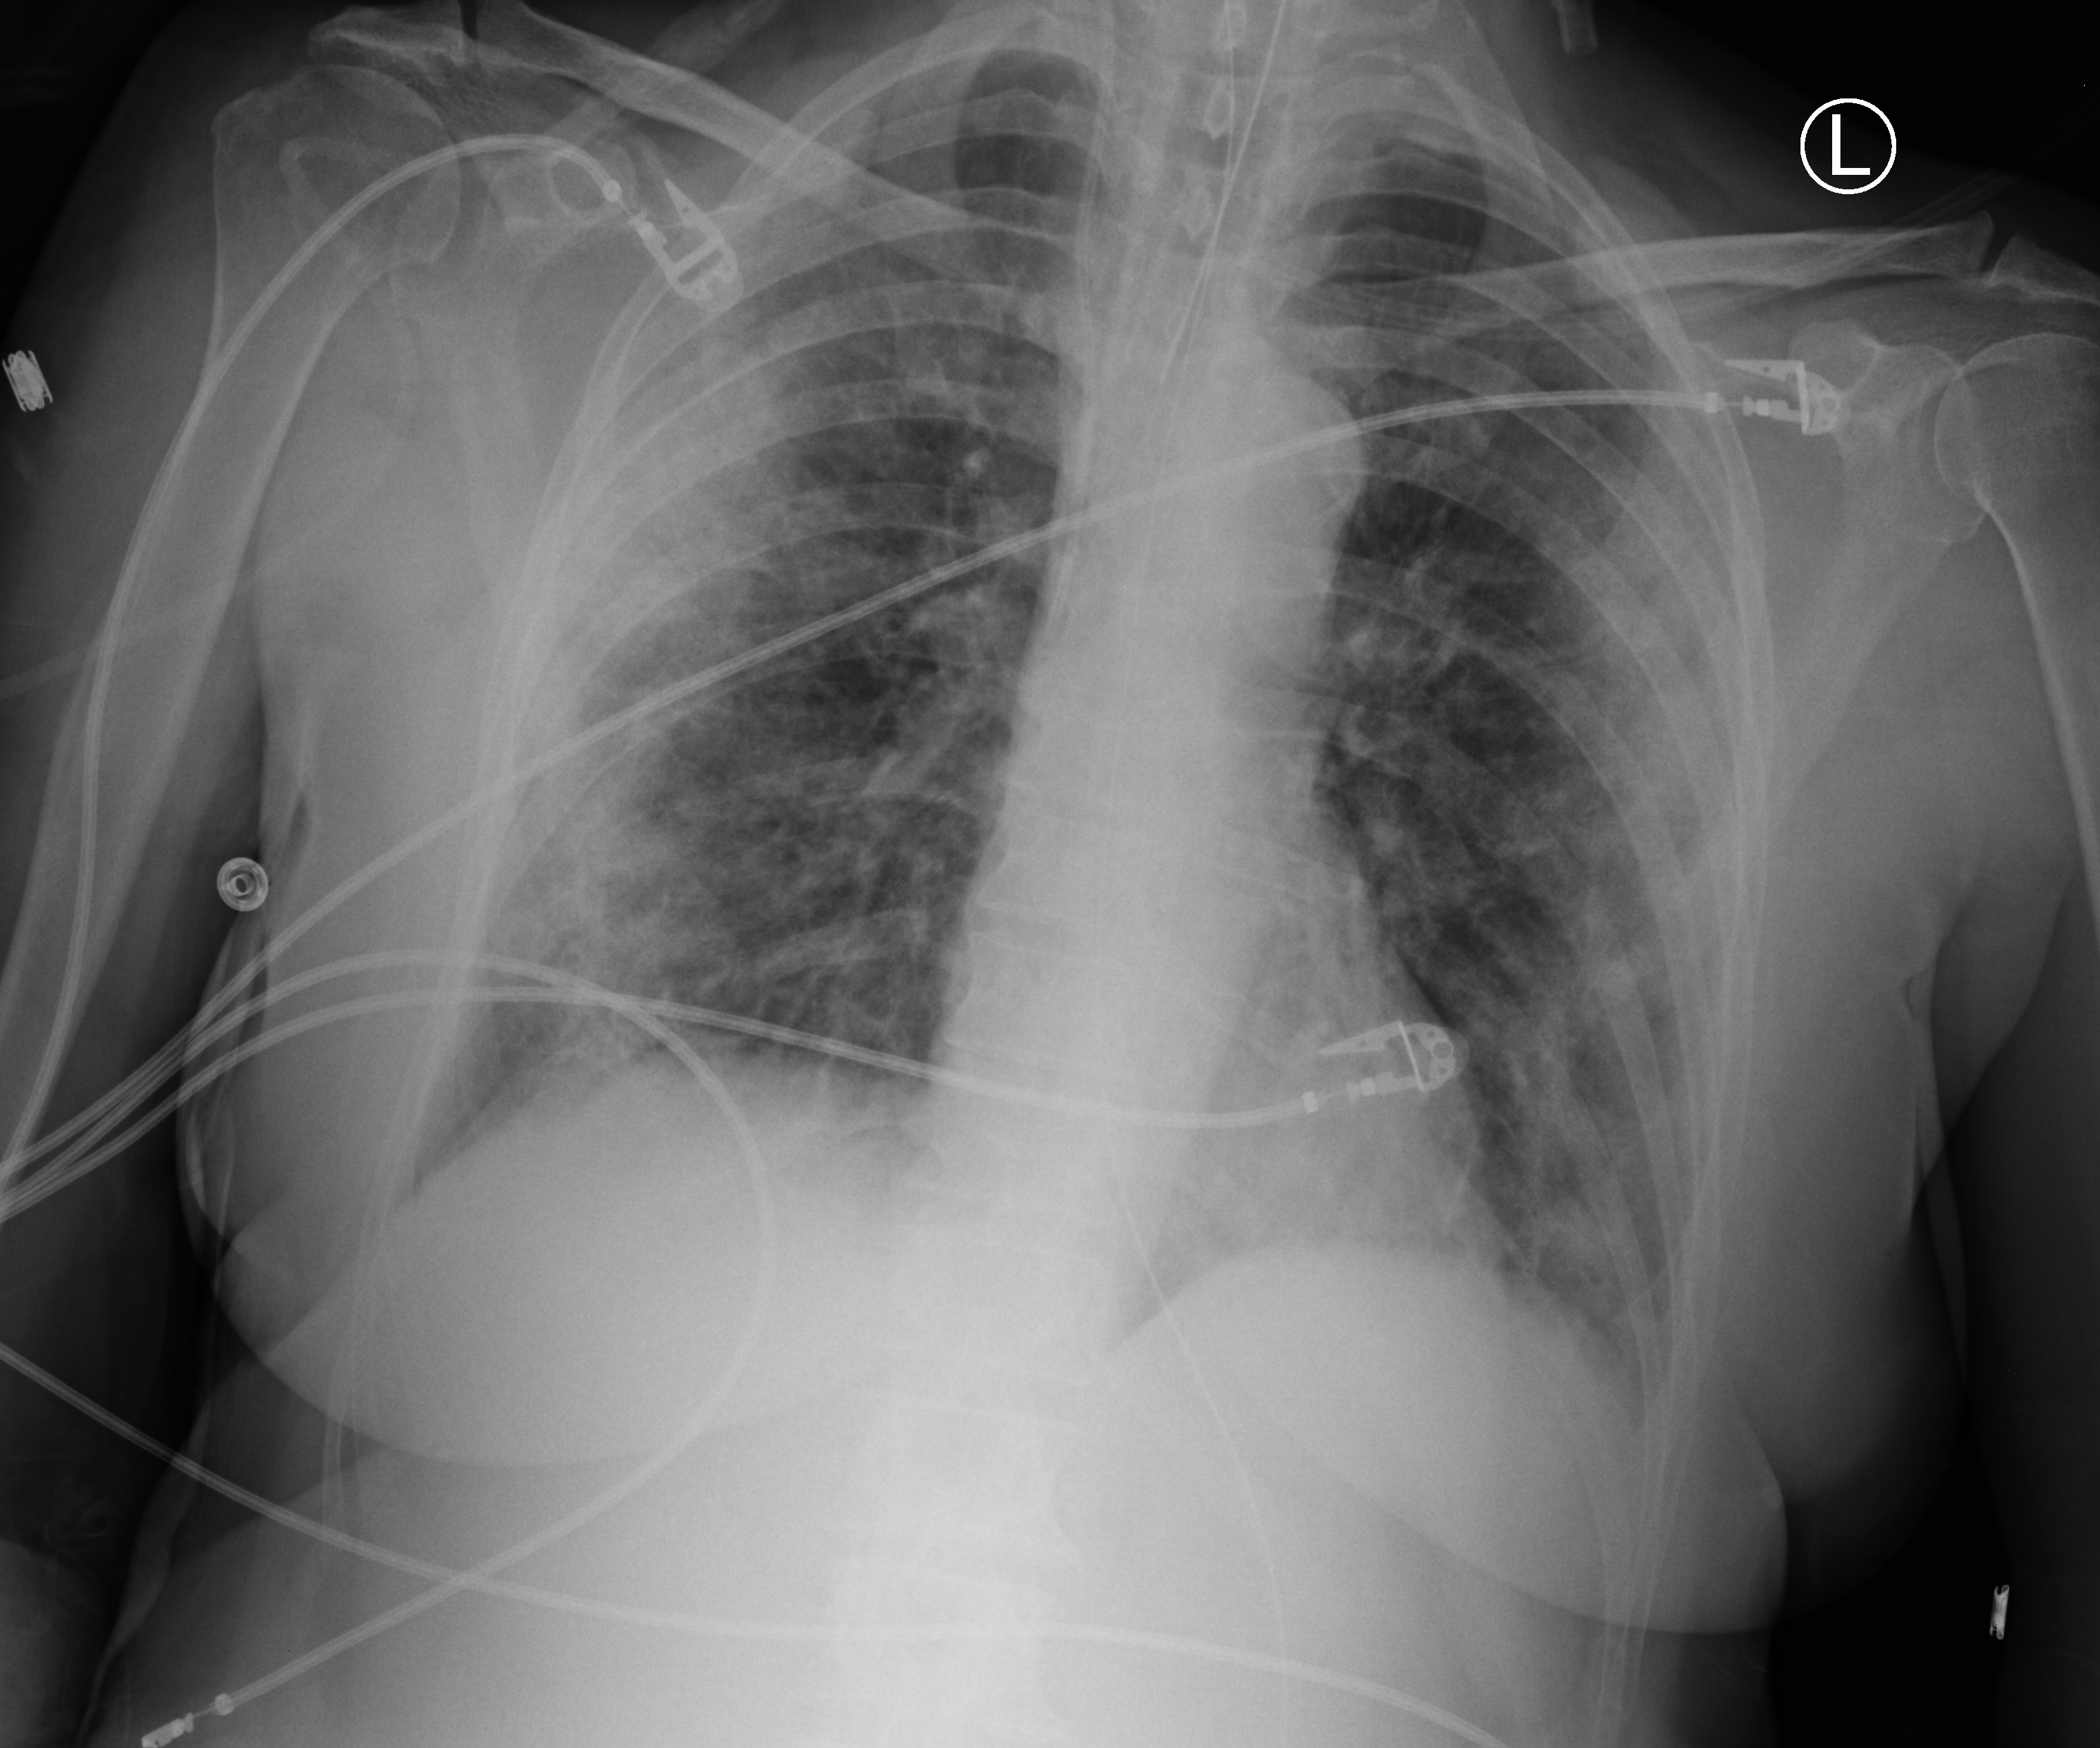
Bedside chest radiograph (computed radiography); anteroposterior (AP) projection. Patient hospitalised with COVID-19; female, aged 60–74 years.
Hospital-stay facts (about this admission, not read from this image; timing relative to this image not recorded): admitted to intensive care during this hospital stay: yes; hypertension (admission record): yes; smoking status (admission record): former.